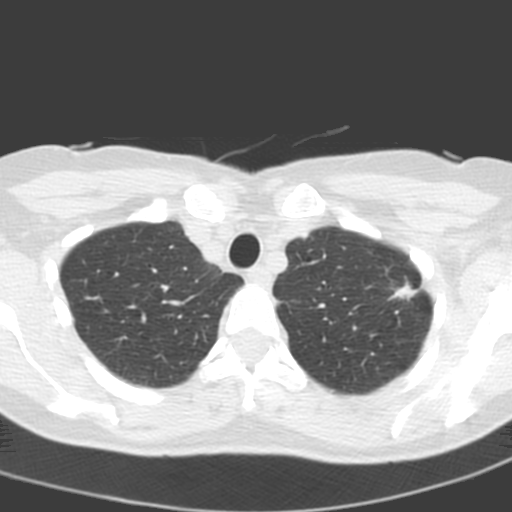
Low-dose screening chest CT, one axial slice. Position 162 of 193 along the scan axis. Lung window (W 1500 / L -600 HU). 3.2 mm slice thickness. 512 × 512 image matrix, field of view 272 × 272 mm.
Annotated regions visible in this slice (expert manual segmentation):
- lesion 1 (tumor, upper lobe of left lung): box from (x=390, y=282) to (x=422, y=300) px